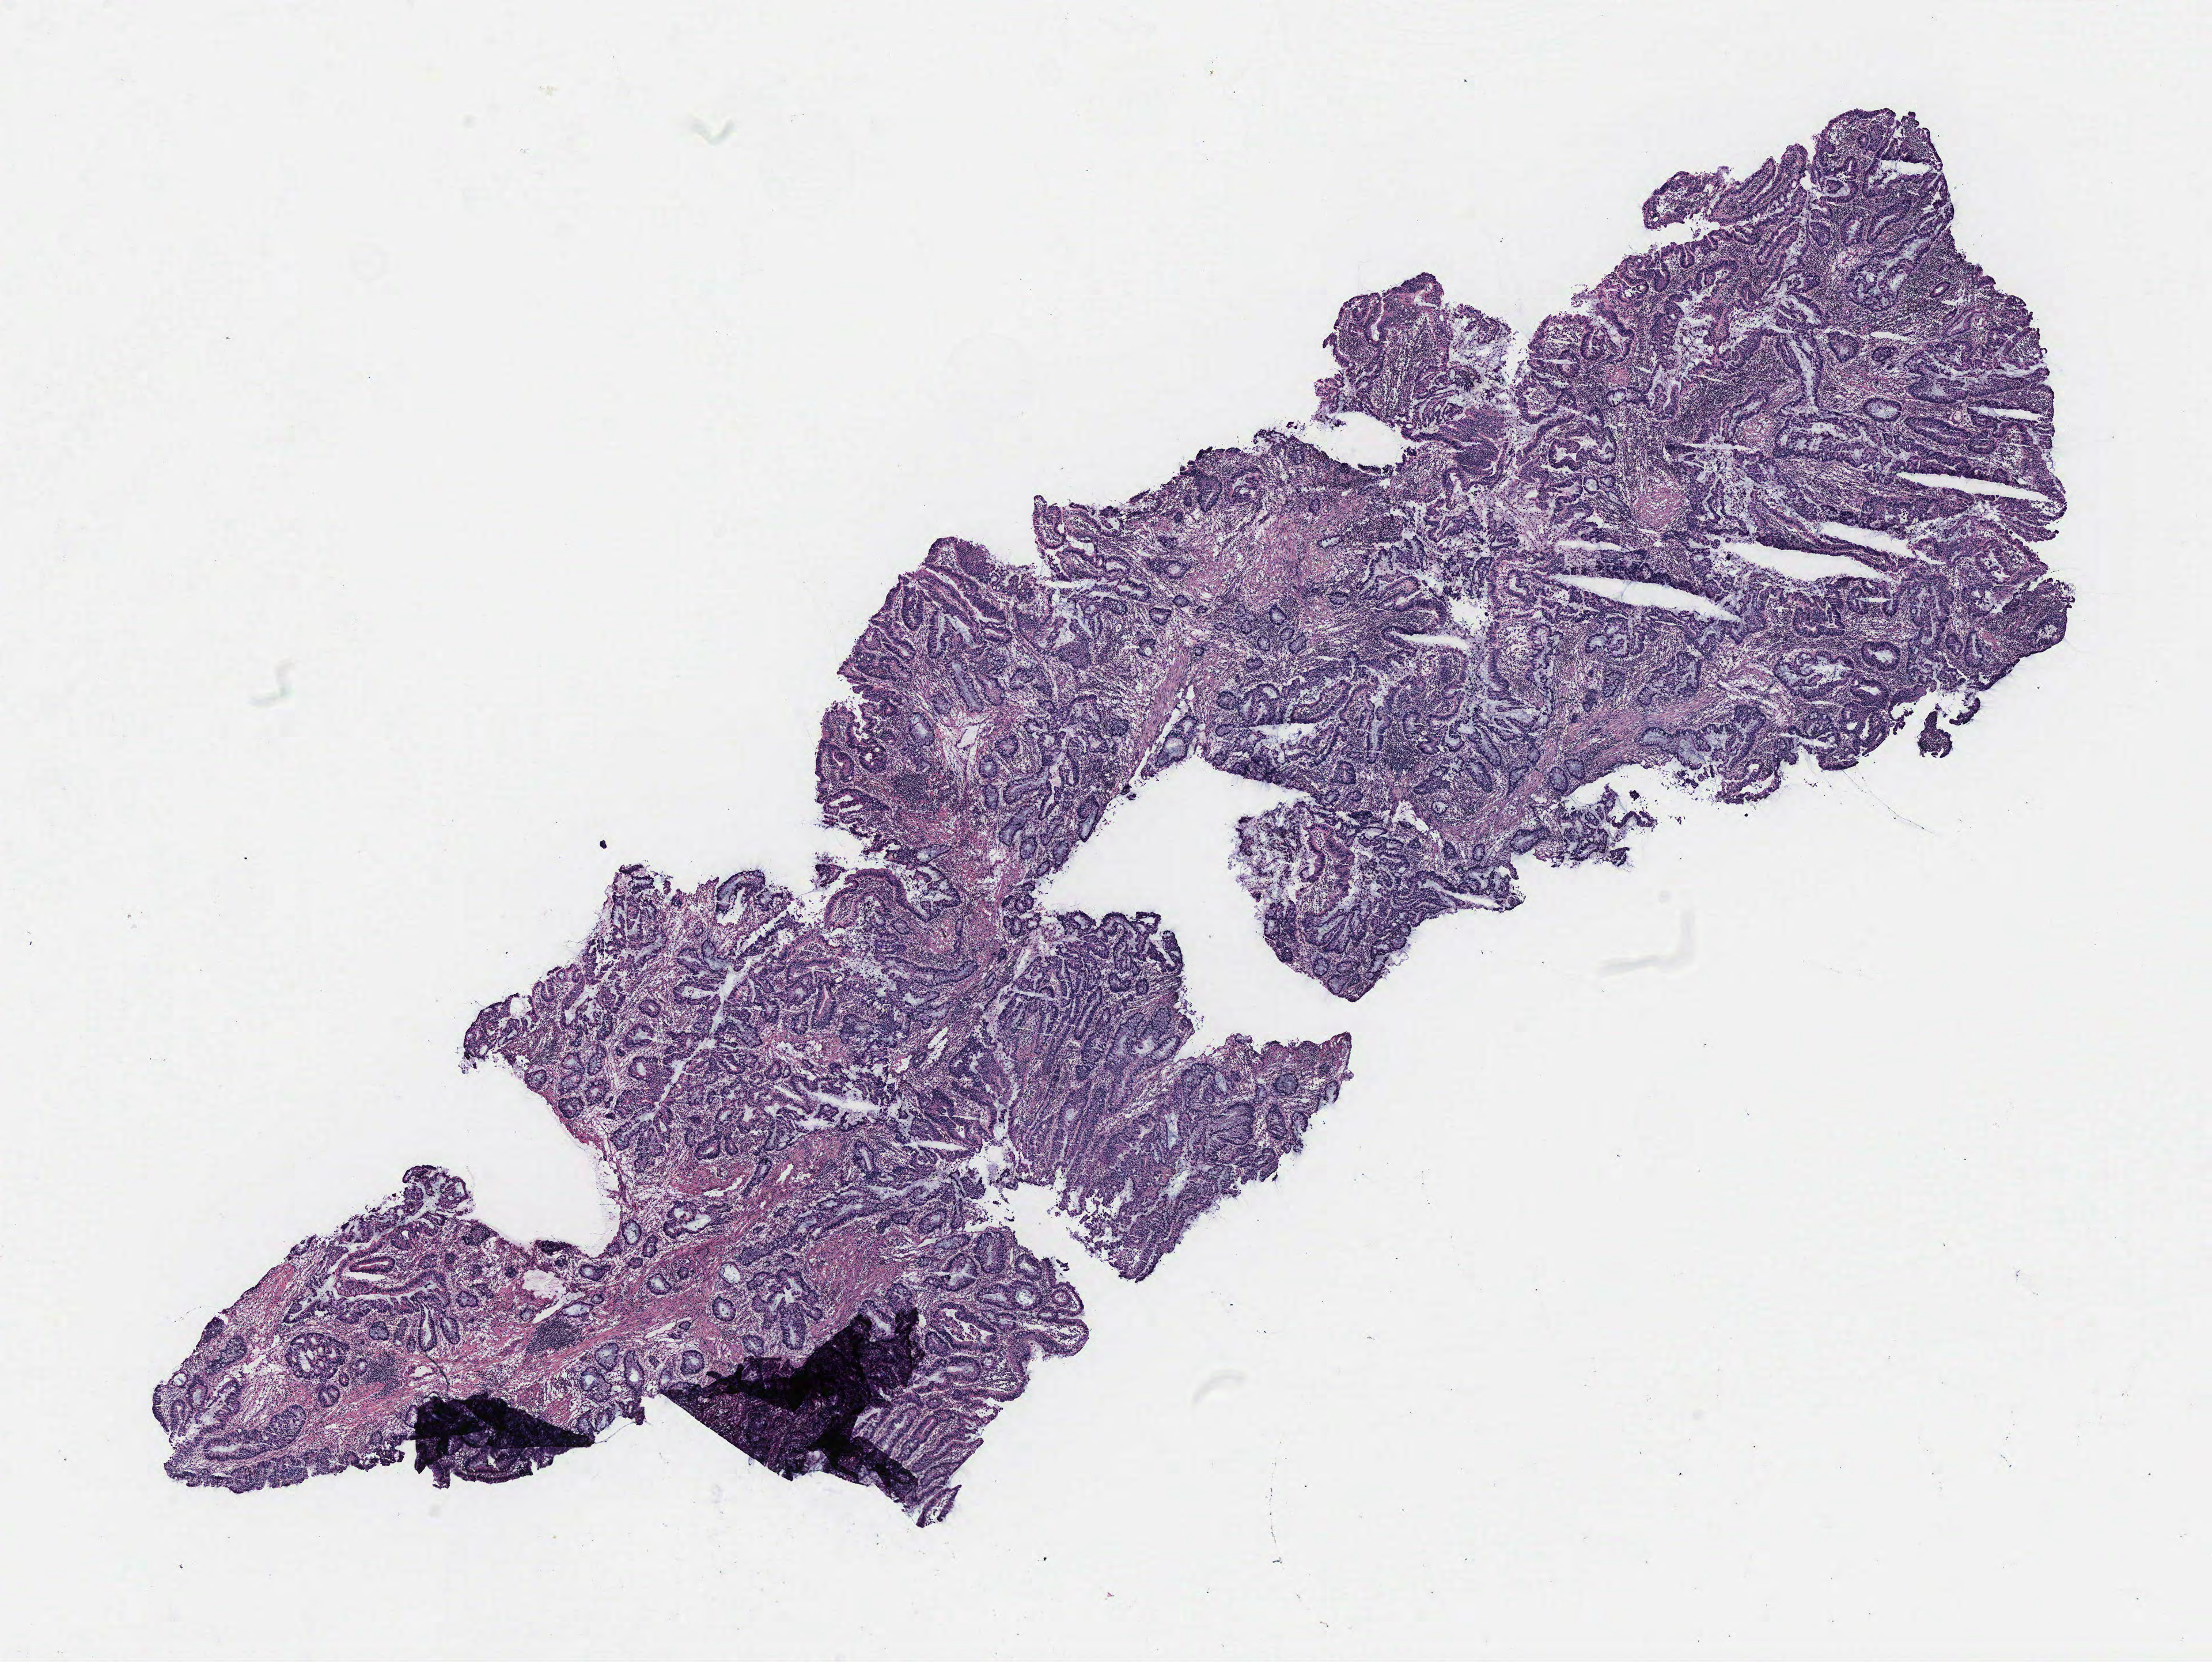
Hematoxylin and eosin (H&E) stained whole-slide image, a low-resolution overview of the entire scanned area, about 15.4 x 11.5 mm (acquisition: 40x scan); colon, normal (non-tumour) tissue. Patient: female, age 55 years.
This section: normal (non-tumour) tissue from the same patient. Patient diagnosis: Adenocarcinoma, NOS.